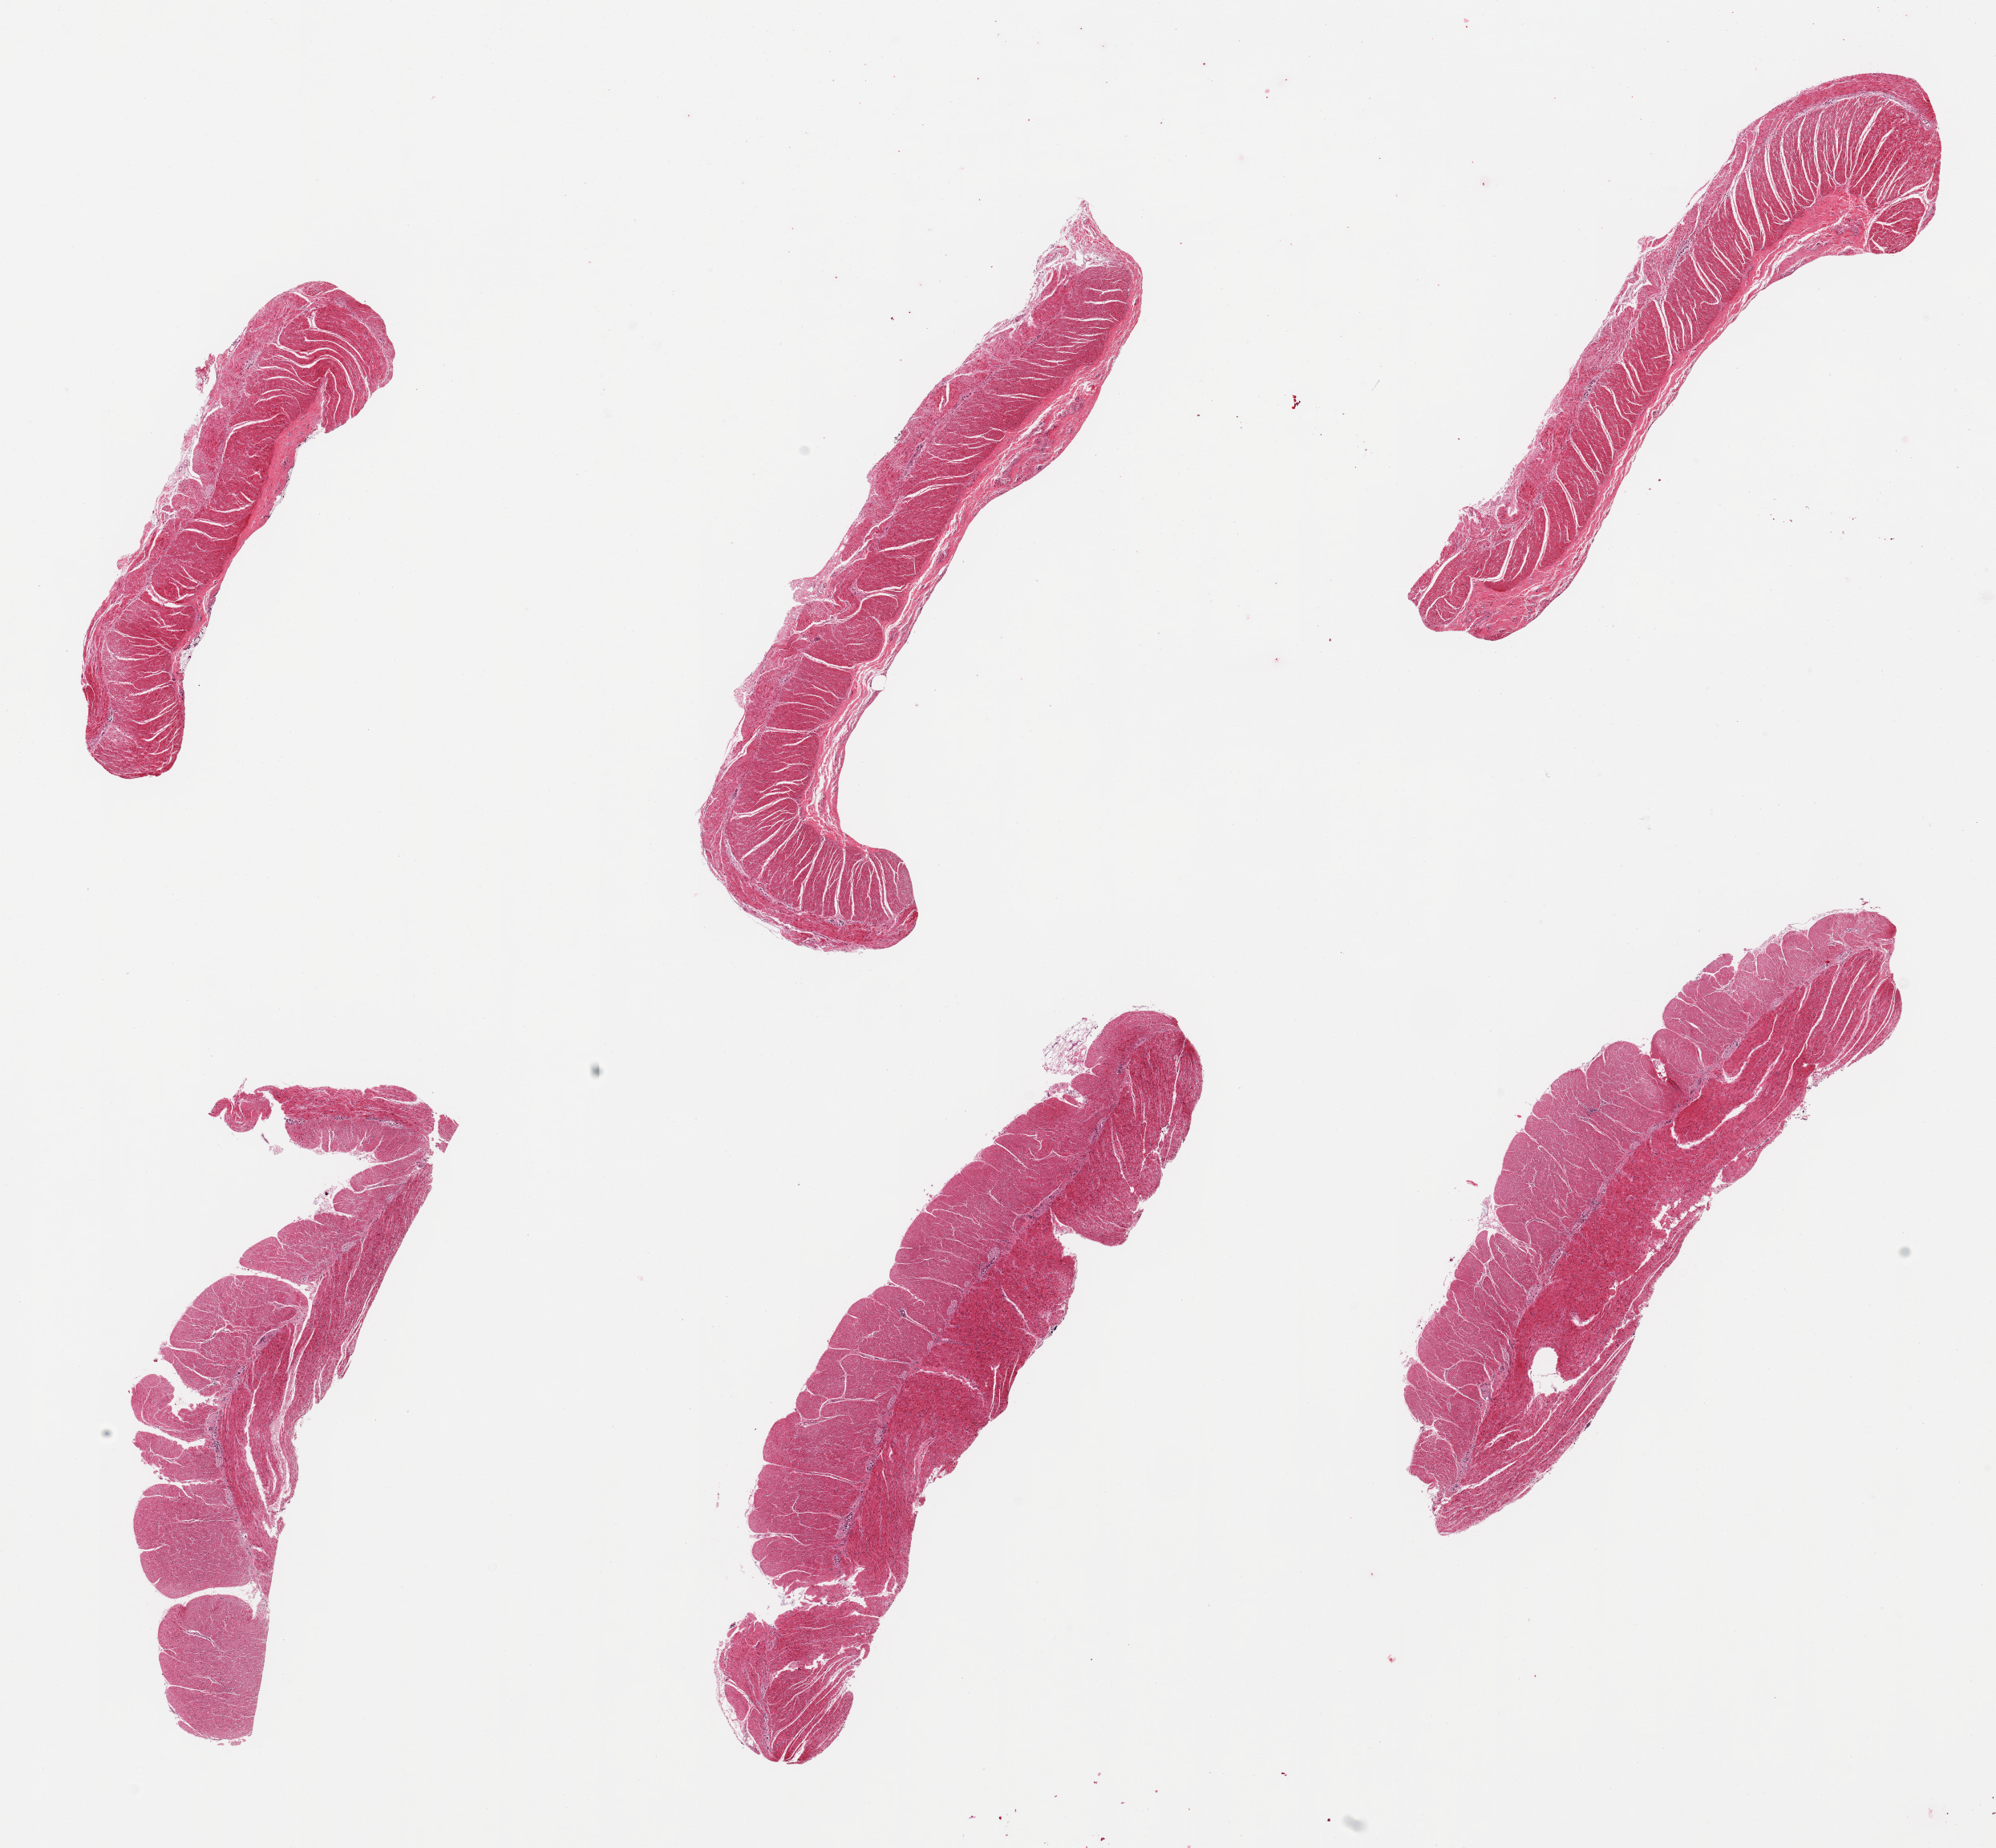
Whole-slide image, hematoxylin and eosin (H&E) stain, whole scanned area (about 19.7 x 18.2 mm, from a 20x scan) shown as a low-resolution overview, PAXgene-fixed paraffin-embedded (PFPE) section, sampled site (target tissue): sigmoid colon, donor tissue sample. Male donor.
Review note (as recorded): 6 pieces; well dissected muscle.